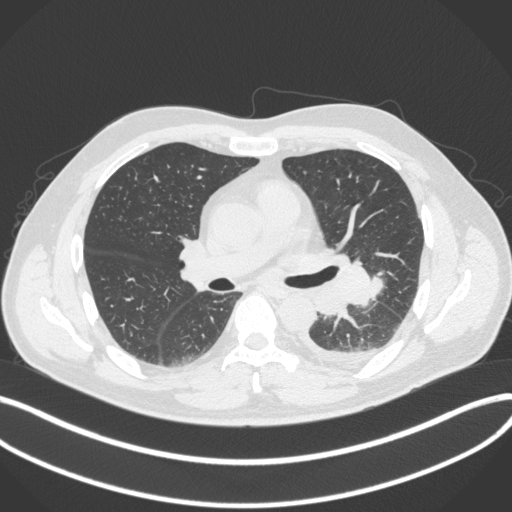
Chest CT, one axial slice. Slice 206 of 350 in the series (ordered by position). 120 kVp. Lung window (W 1500 / L -600 HU). 512 × 512 image matrix. Patient: male, 58 years. Case-level facts recorded for this patient, not image findings: clinical TNM (as recorded): T3 N1 M1b; histopathological grade: G3.
Outlined on this slice (rectangle marked by the reading radiologist):
- lung tumour (recorded histology: small cell carcinoma): bounding box <305,260,387,313> (left, top, right, bottom; pixels)